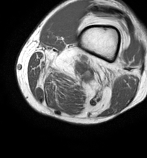
MRI of an extremity soft-tissue mass, one axial slice; slice 17 of 86 in the series (ordered by position); MR volume resampled by the dataset authors to the PET/CT grid (not the native acquisition matrix); 3.27 mm slice thickness; 147 × 158 image matrix, field of view 144 × 154 mm. Male patient. From the clinical record (not read from this slice): histological type: undifferentiated pleomorphic liposarcoma; grade: high; site of the primary tumour: left thigh.
Annotated regions visible in this slice (expert contour drawn on MRI and transferred to this co-registered scan by the dataset authors):
- gross tumour volume including surrounding oedema: bounding box (x1, y1, x2, y2) in pixels: (37, 54, 115, 91)